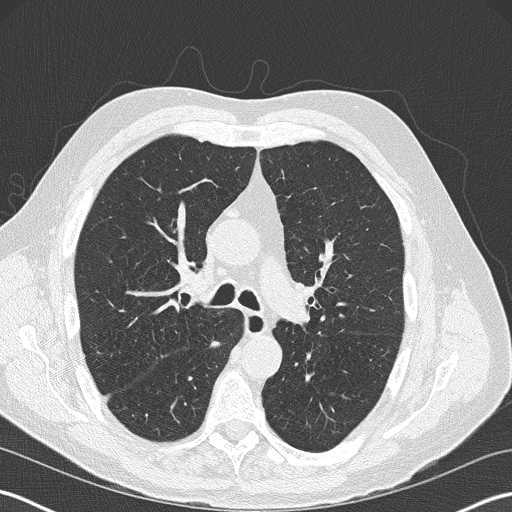
Low-dose screening chest CT, one axial slice; slice 122 of 199 in the series (ordered by position); reconstruction kernel B50f; 120 kVp; lung window (W 1500 / L -600 HU); 2 mm slice thickness; 512 × 512 image matrix, field of view 350 × 350 mm.
Annotated regions visible in this slice (expert manual segmentation):
- lesion 1 (tumor, upper lobe of right lung): box from (x=156, y=353) to (x=174, y=369) px